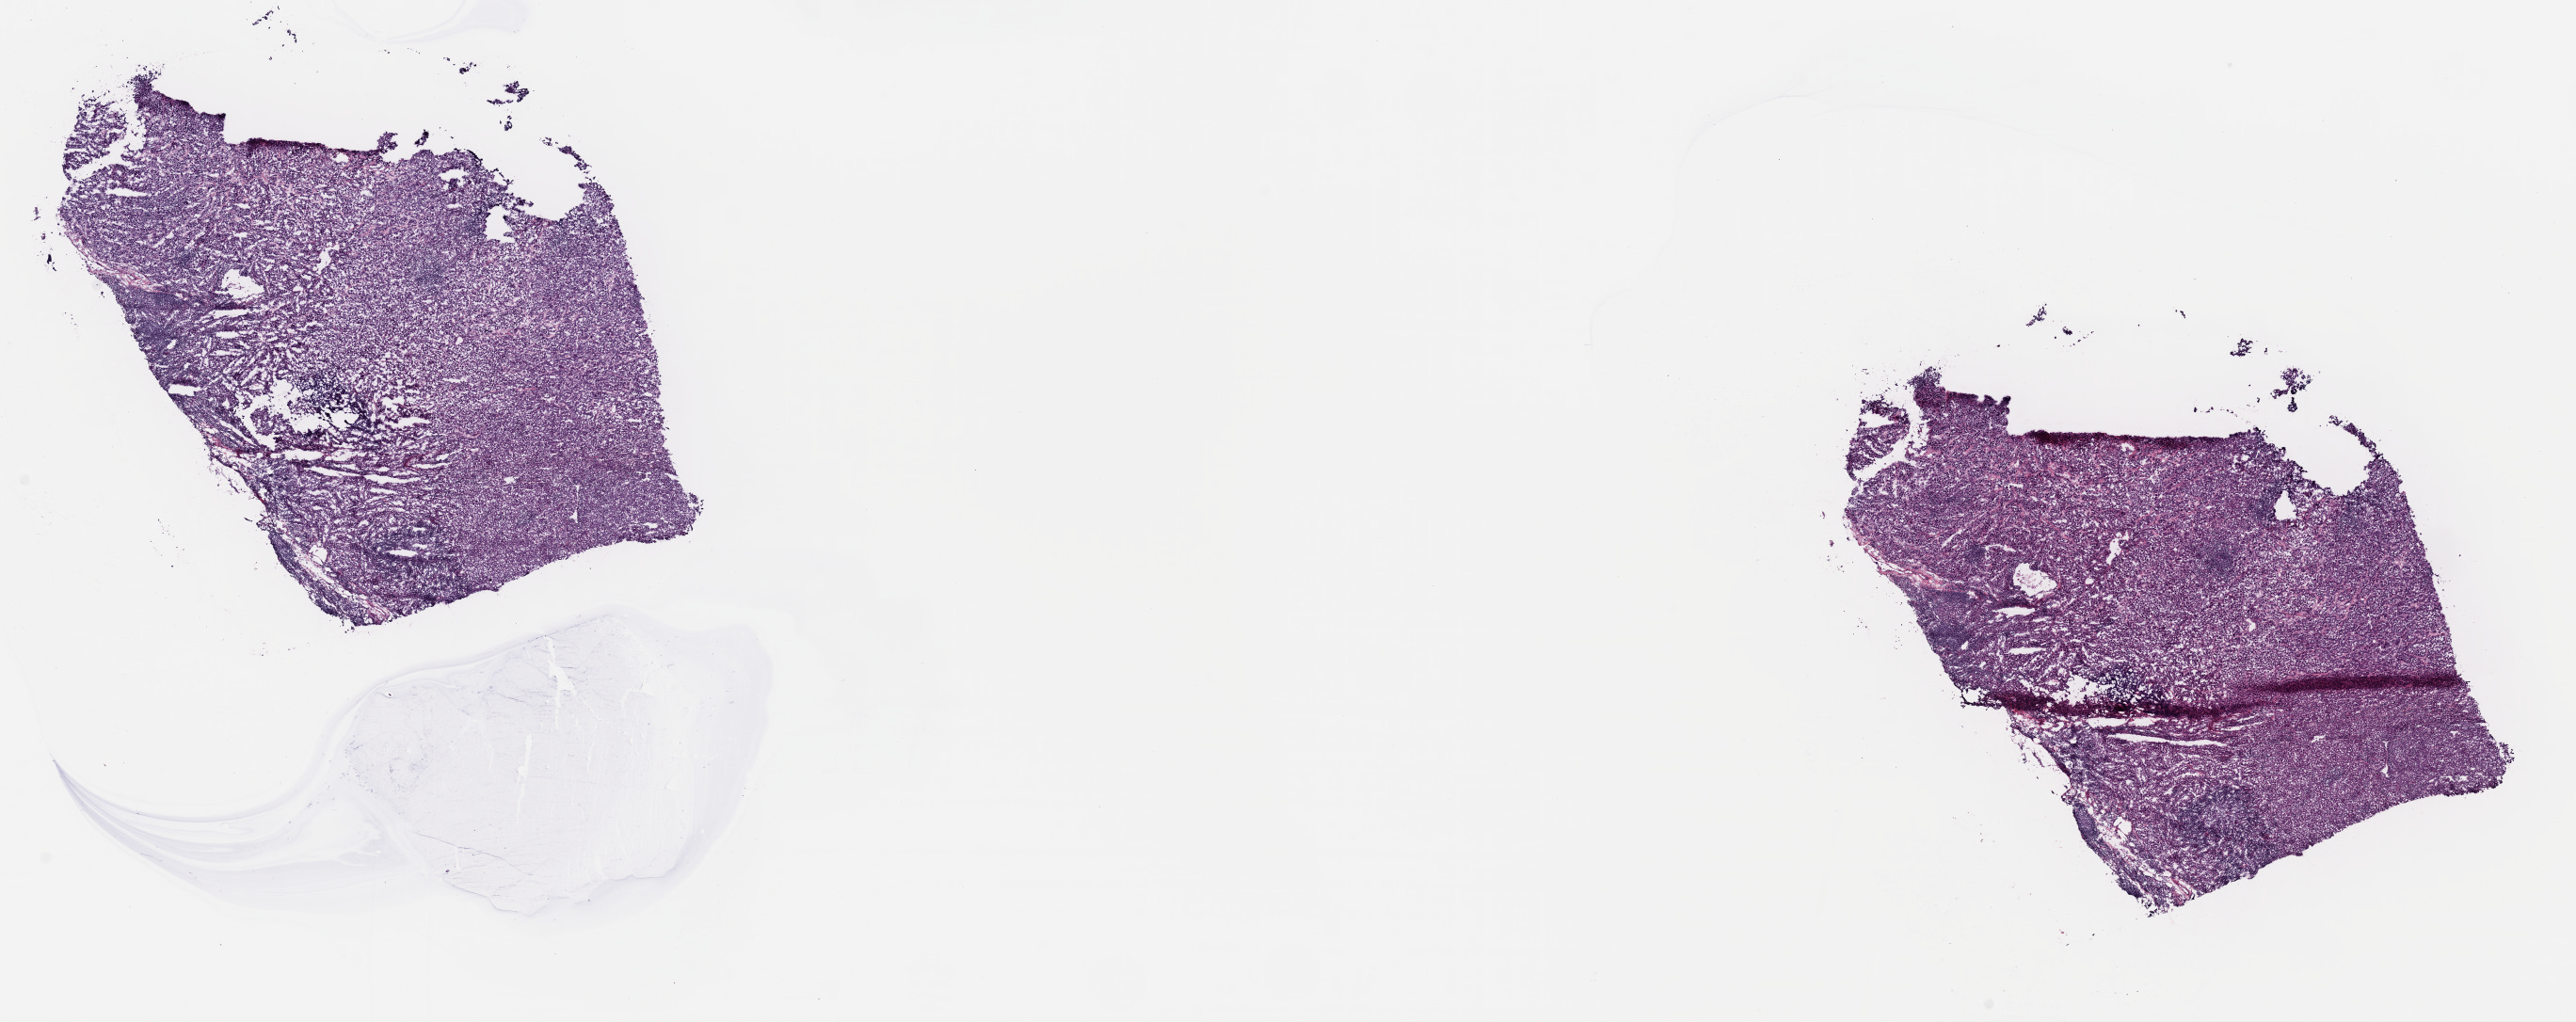
Whole-slide histology image, H&E-stained — shown as a low-resolution overview of the whole scanned area (about 21.6 x 8.6 mm, from a 40x scan), frozen section, metastatic tumour sample, sampled site not recorded. Patient: female, age at initial diagnosis 40 years. Composition of this section per pathologist review: tumour cells 100%, tumour nuclei 98%, normal cells 0%, stromal cells 0%, necrosis 0%. Infiltration values recorded for this section: lymphocyte infiltration 0%, monocyte infiltration 0%, neutrophil infiltration 0%.
This section: metastatic tumour tissue. Patient diagnosis: Malignant melanoma, NOS.